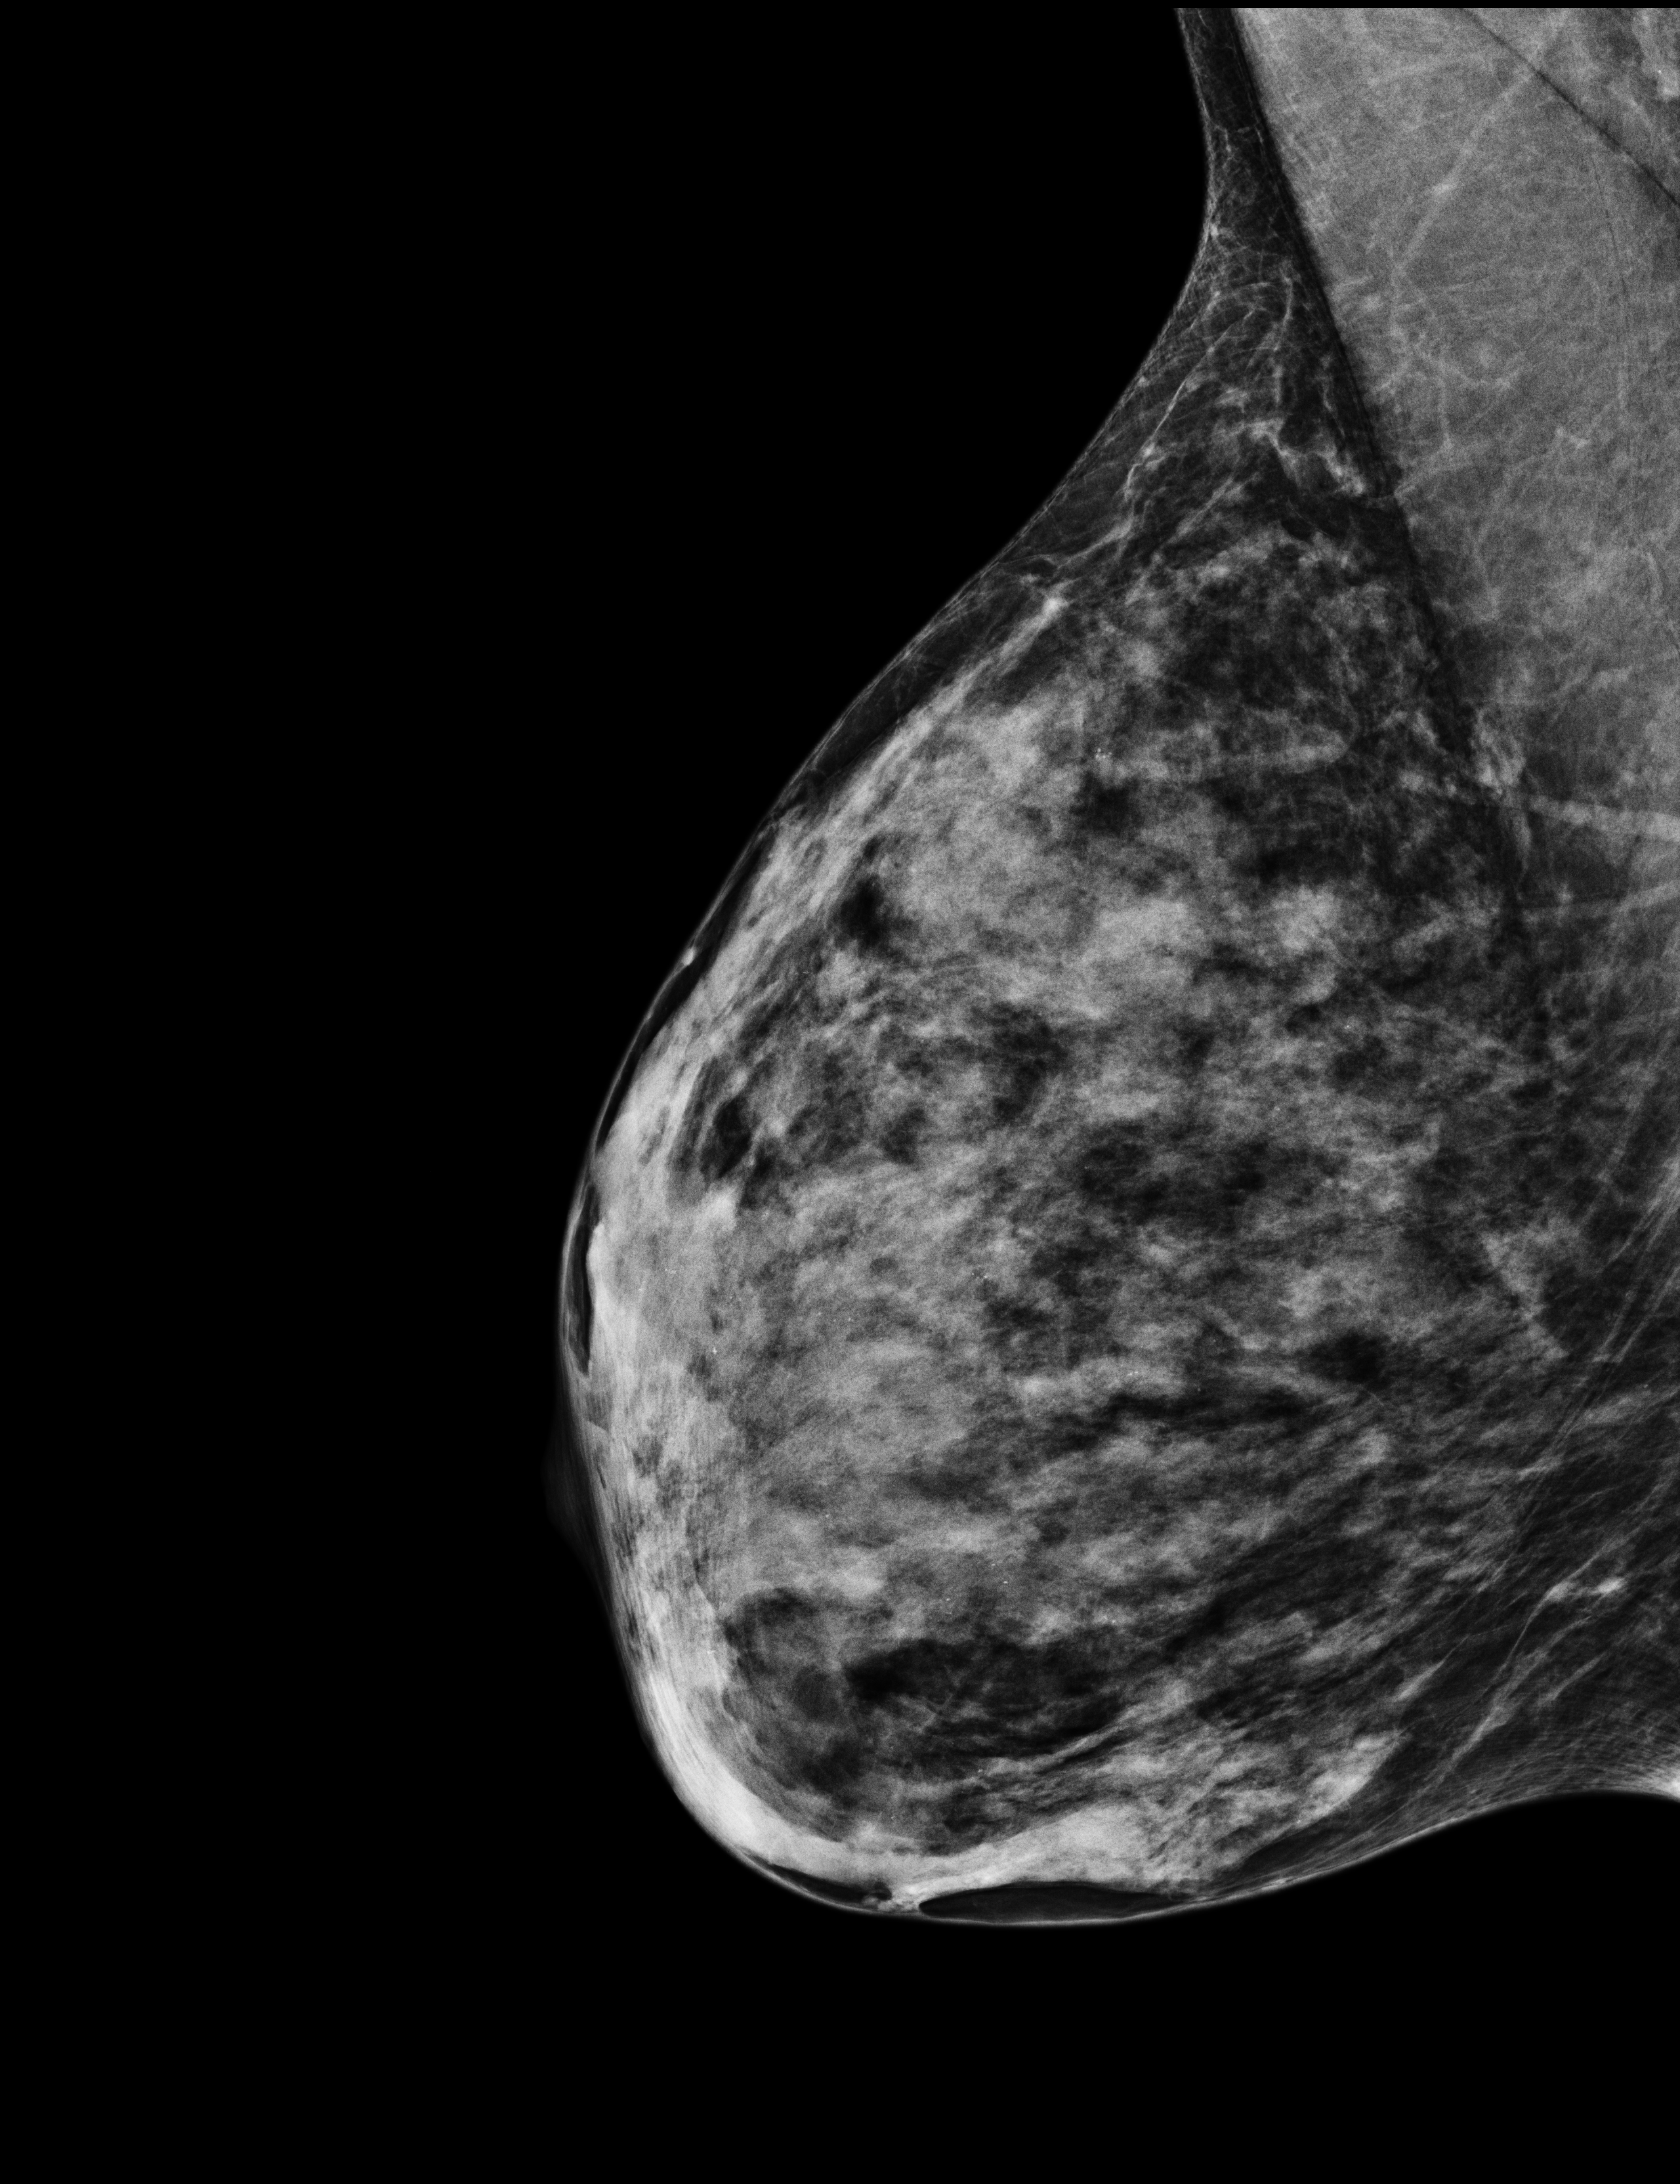
Full-field digital mammogram (FFDM); right breast; mediolateral oblique (MLO) view; annual screening mammography examination; compressed breast thickness 36 mm. Patient: female, 43 years.
- breast density at the screening exam (both breasts): extremely dense (BI-RADS density category d)
- final BI-RADS assessment for this screening round (tomosynthesis exam, both breasts): category 2
- recall: no recall after this screen